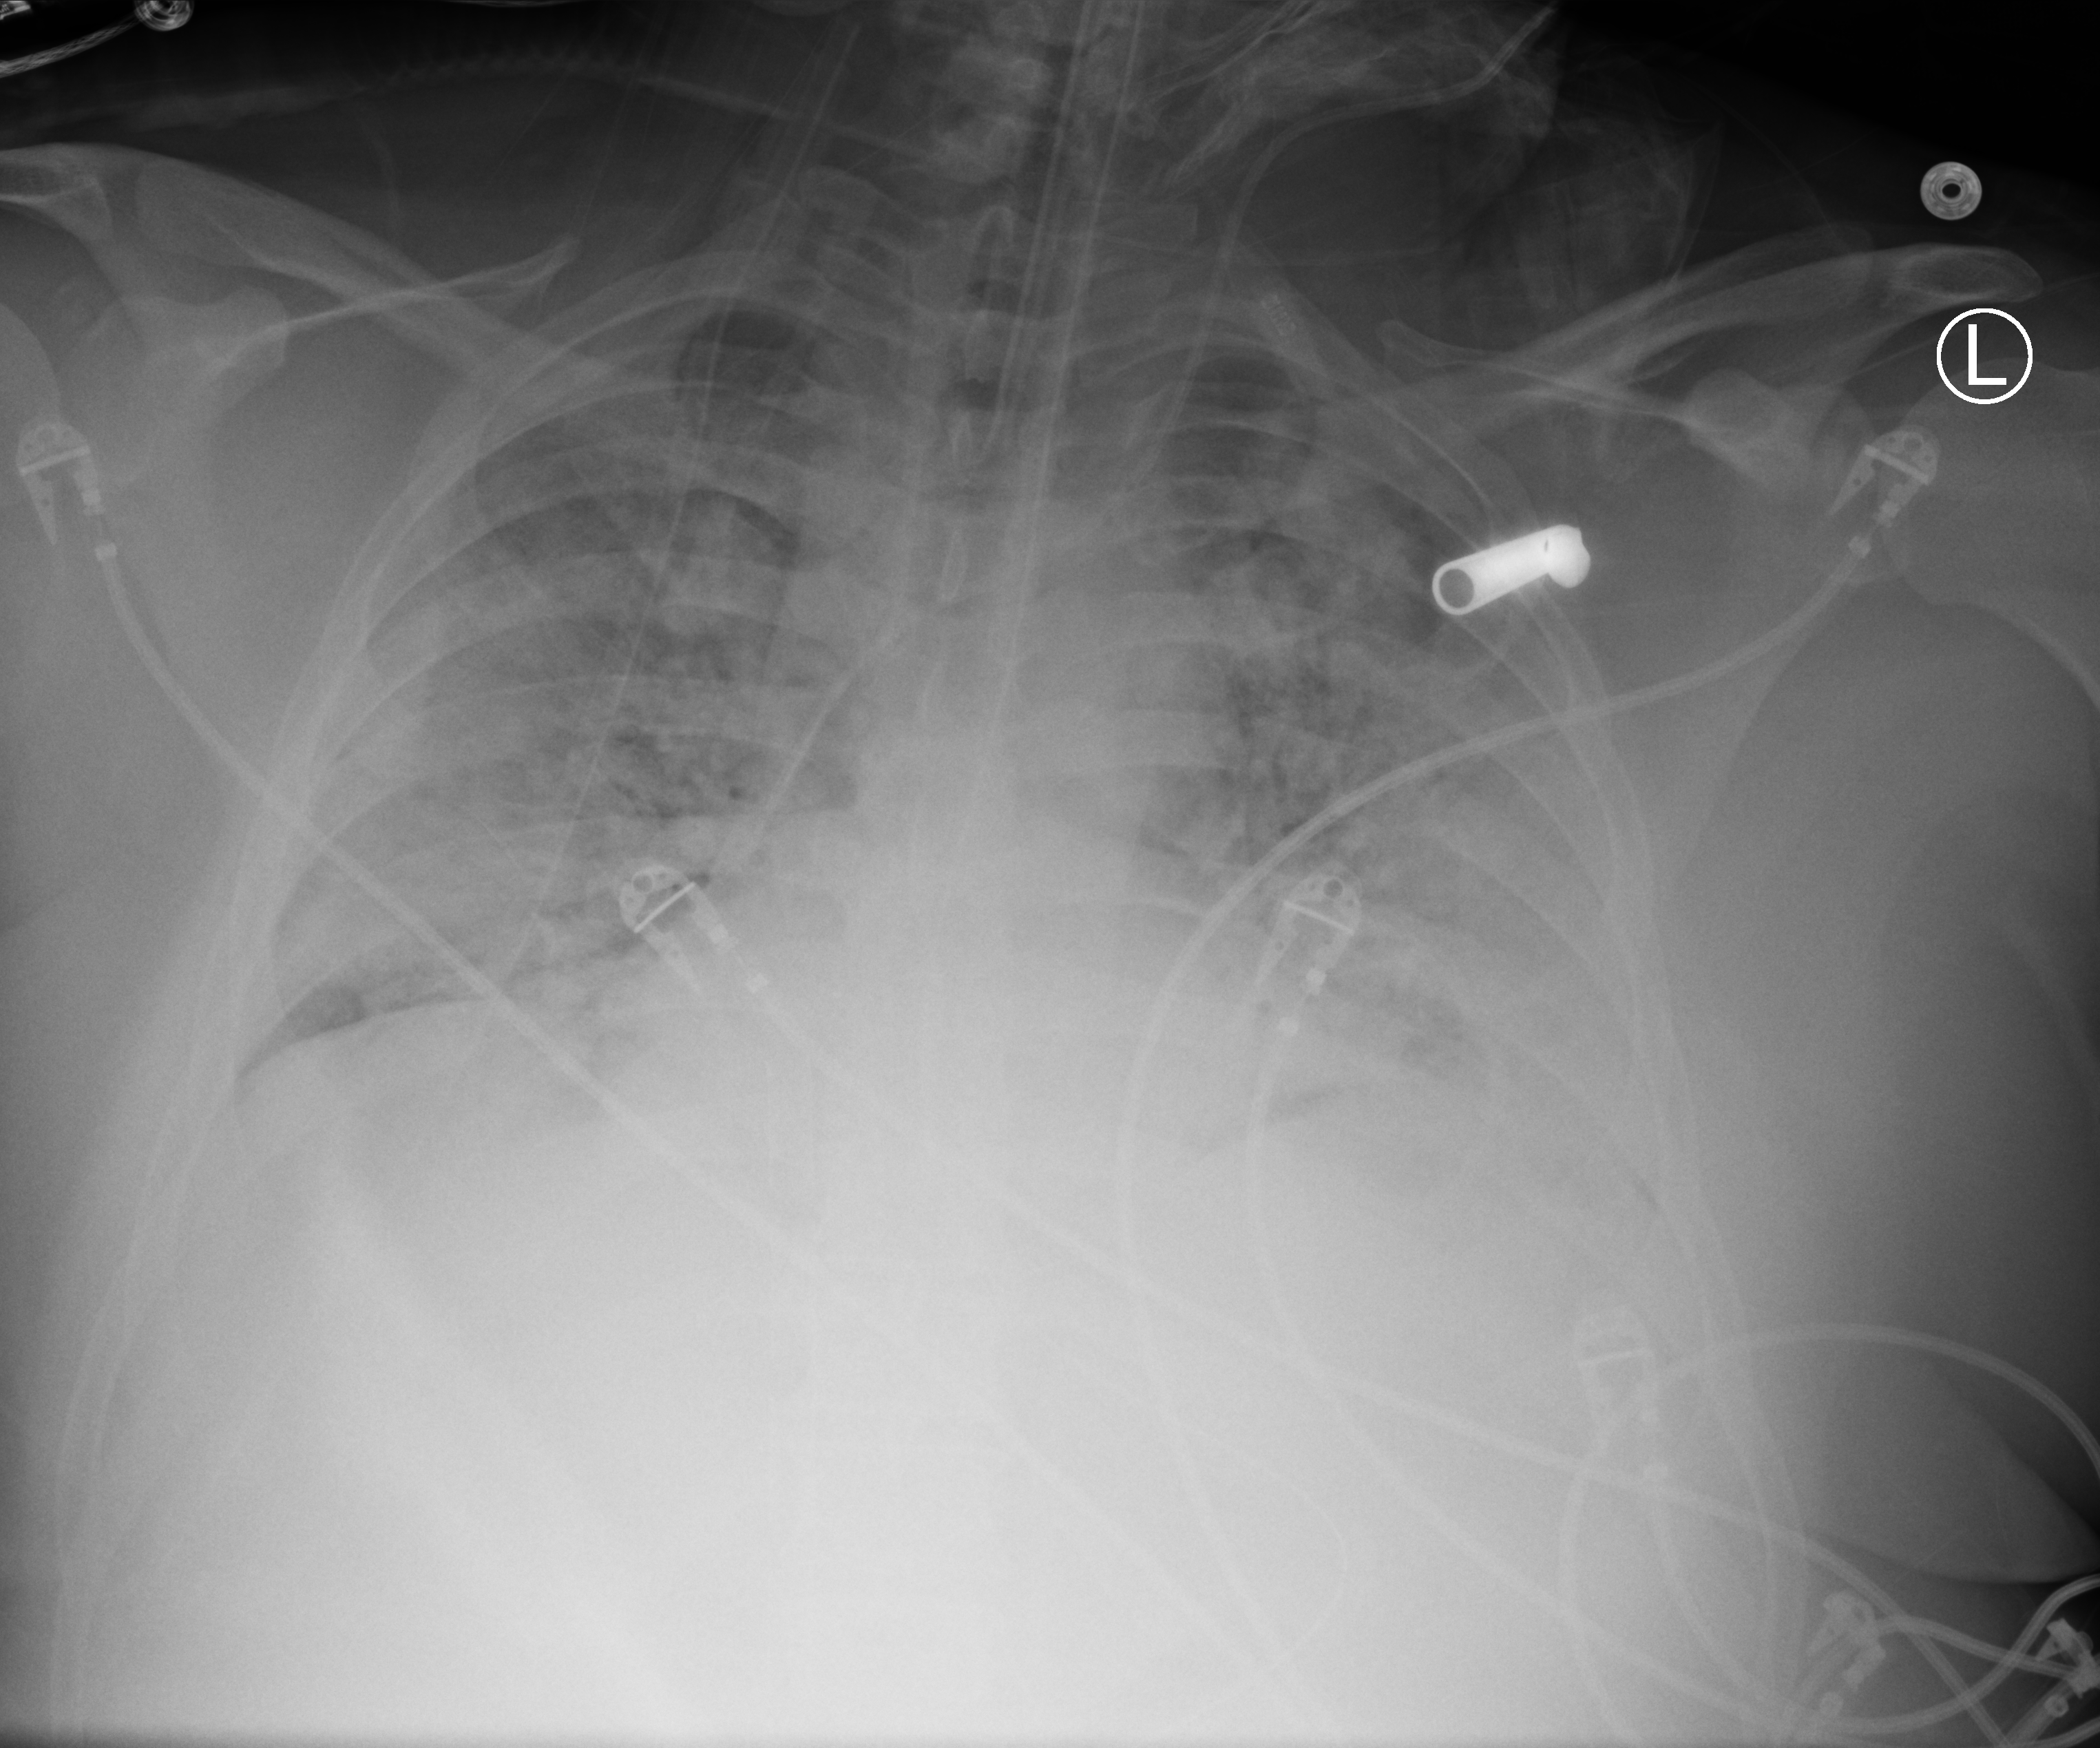
Portable chest radiograph; anteroposterior (AP) projection. Adult patient hospitalised with COVID-19, age 18–59 years.
From the hospital-stay record, not from the radiograph (when in the stay this image was taken is not recorded):
- mechanically ventilated during this hospital stay: yes
- admitted to intensive care during this hospital stay: yes
- length of hospital stay: 15 days